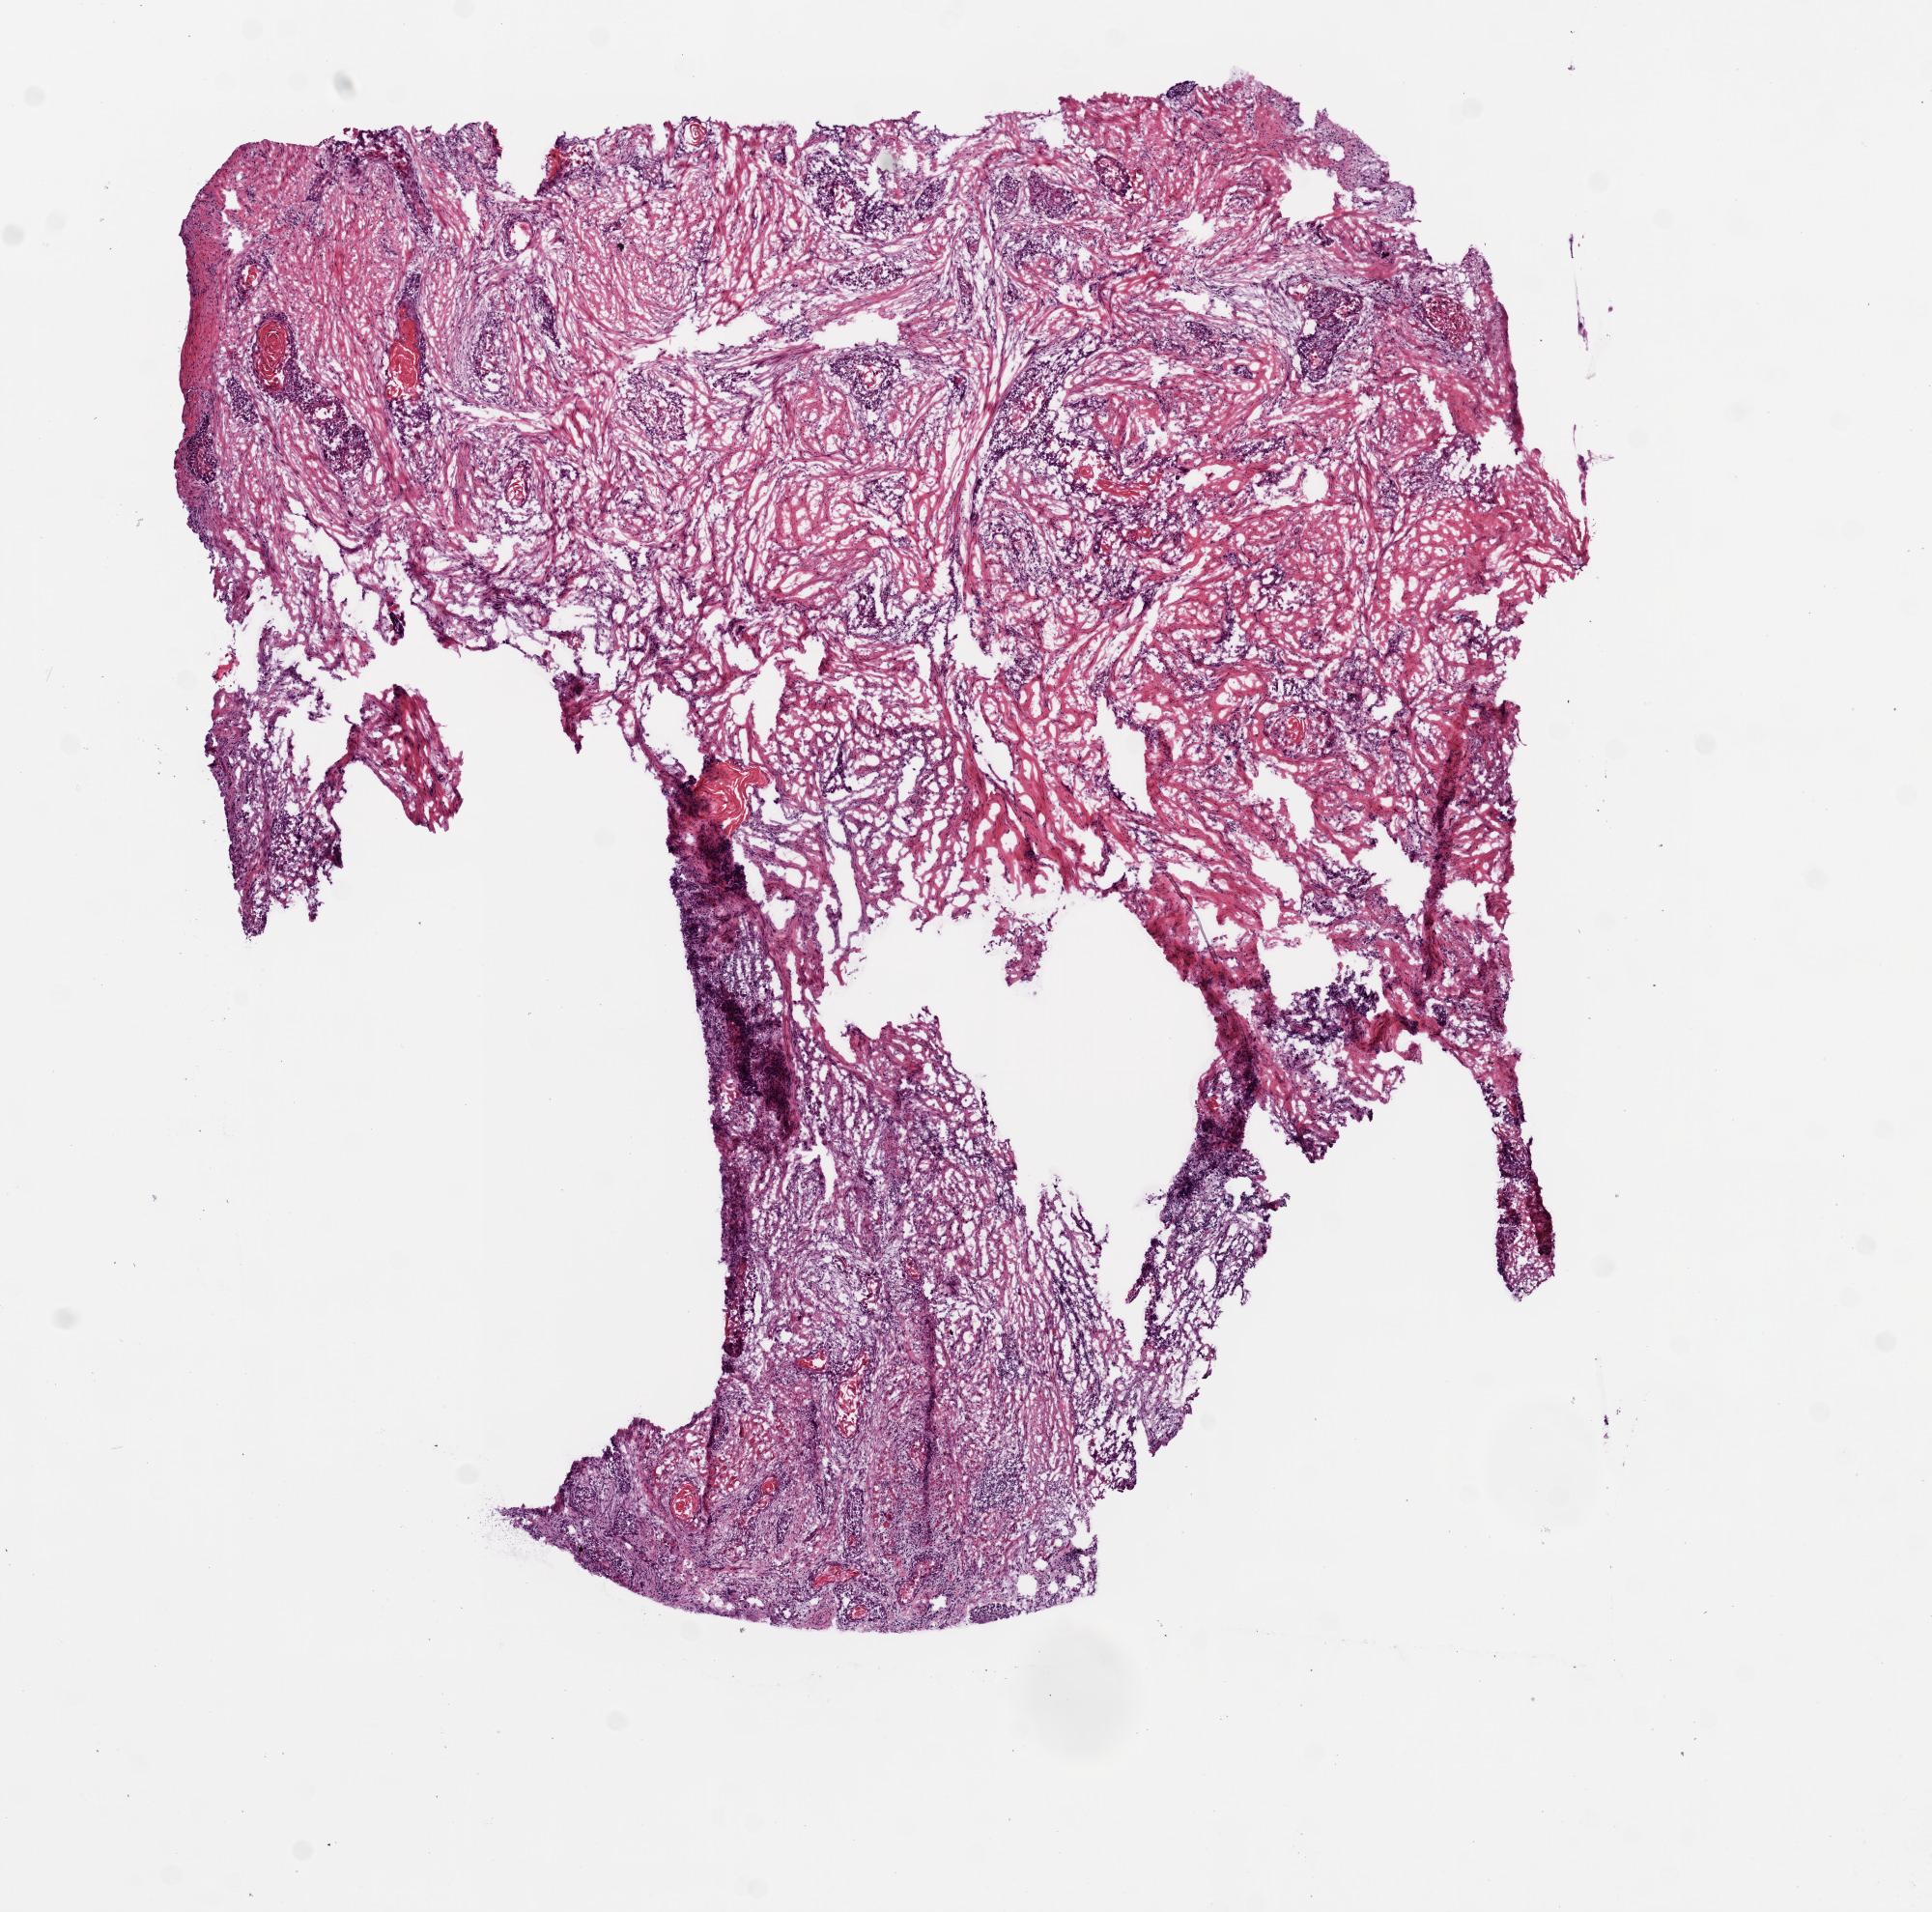
Whole-slide histology image, H&E, shown as a low-resolution overview of the whole scanned area (about 8.0 x 7.9 mm, acquisition: 20x scan); frozen section from the top of the tissue portion; primary tumour sample from the head and neck. Patient: male, age at initial diagnosis 56 years. Histologic grade: G2 (moderately differentiated). Composition of this section per pathologist review: tumour cells 70%, tumour nuclei 75%, normal cells 0%, stromal cells 30%, necrosis 0%.
Histologic diagnosis: Squamous cell carcinoma, NOS. TNM: T3 N2b. AJCC pathologic stage: IVA (7th edition).